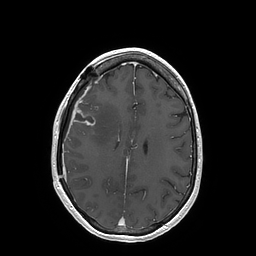
Brain MRI from a brain-tumour surgery series, one axial slice. Slice 64 of 202 in the series (ordered by position). T1-weighted post-contrast. 1 mm slice thickness. 256 × 256 image matrix, field of view 250 × 250 mm. Case-level facts recorded for this patient, not image findings: histopathology: Glioblastoma; WHO grade: 4; IDH mutation: no; tumour location: Right Insular.
Annotated regions visible in this slice (manually delineated by an expert):
- tumour: bounding box <73,108,95,126> (left, top, right, bottom; pixels)